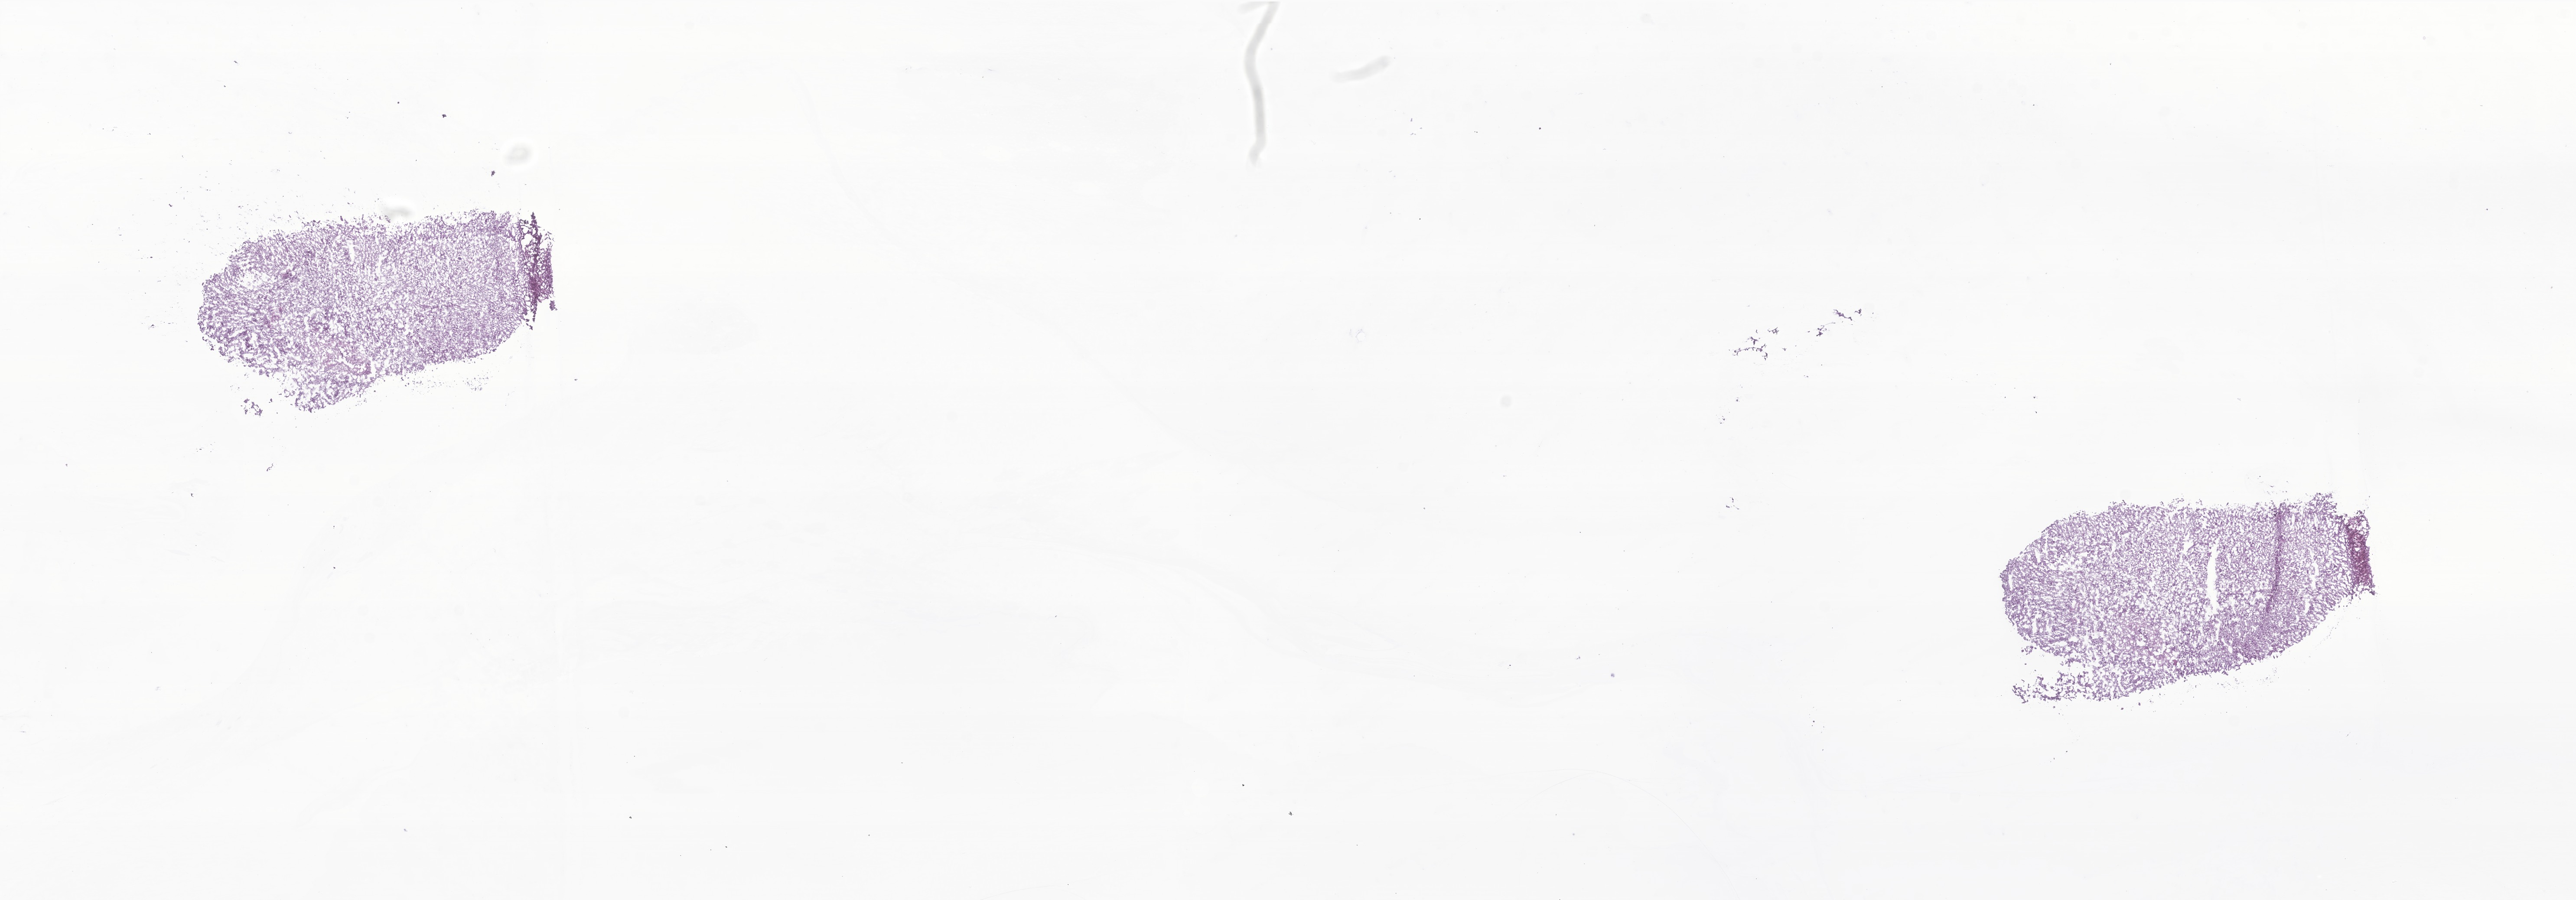
Whole-slide image, H&E stain of tumor tissue from the brain, whole scanned area (about 25.1 x 8.8 mm) shown as a low-resolution overview, frozen section (OCT-embedded). Female patient, age 378 days (about 1.0 years).
- diagnosis (ICD-O-3 morphology term): Astrocytoma, NOS